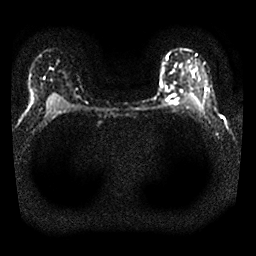
Breast MRI, one axial slice; slice 21 of 25 in the series (ordered by position); diffusion-weighted series; image 2 of 4 stored at this slice position (different b-values; order by instance number); 1.5 T; 4 mm slice thickness; 256 × 256 image matrix, field of view 310 × 310 mm. Female patient.
Outlined on this slice (expert manual segmentation):
- tumour on diffusion-weighted imaging: box from (x=168, y=94) to (x=179, y=102) px